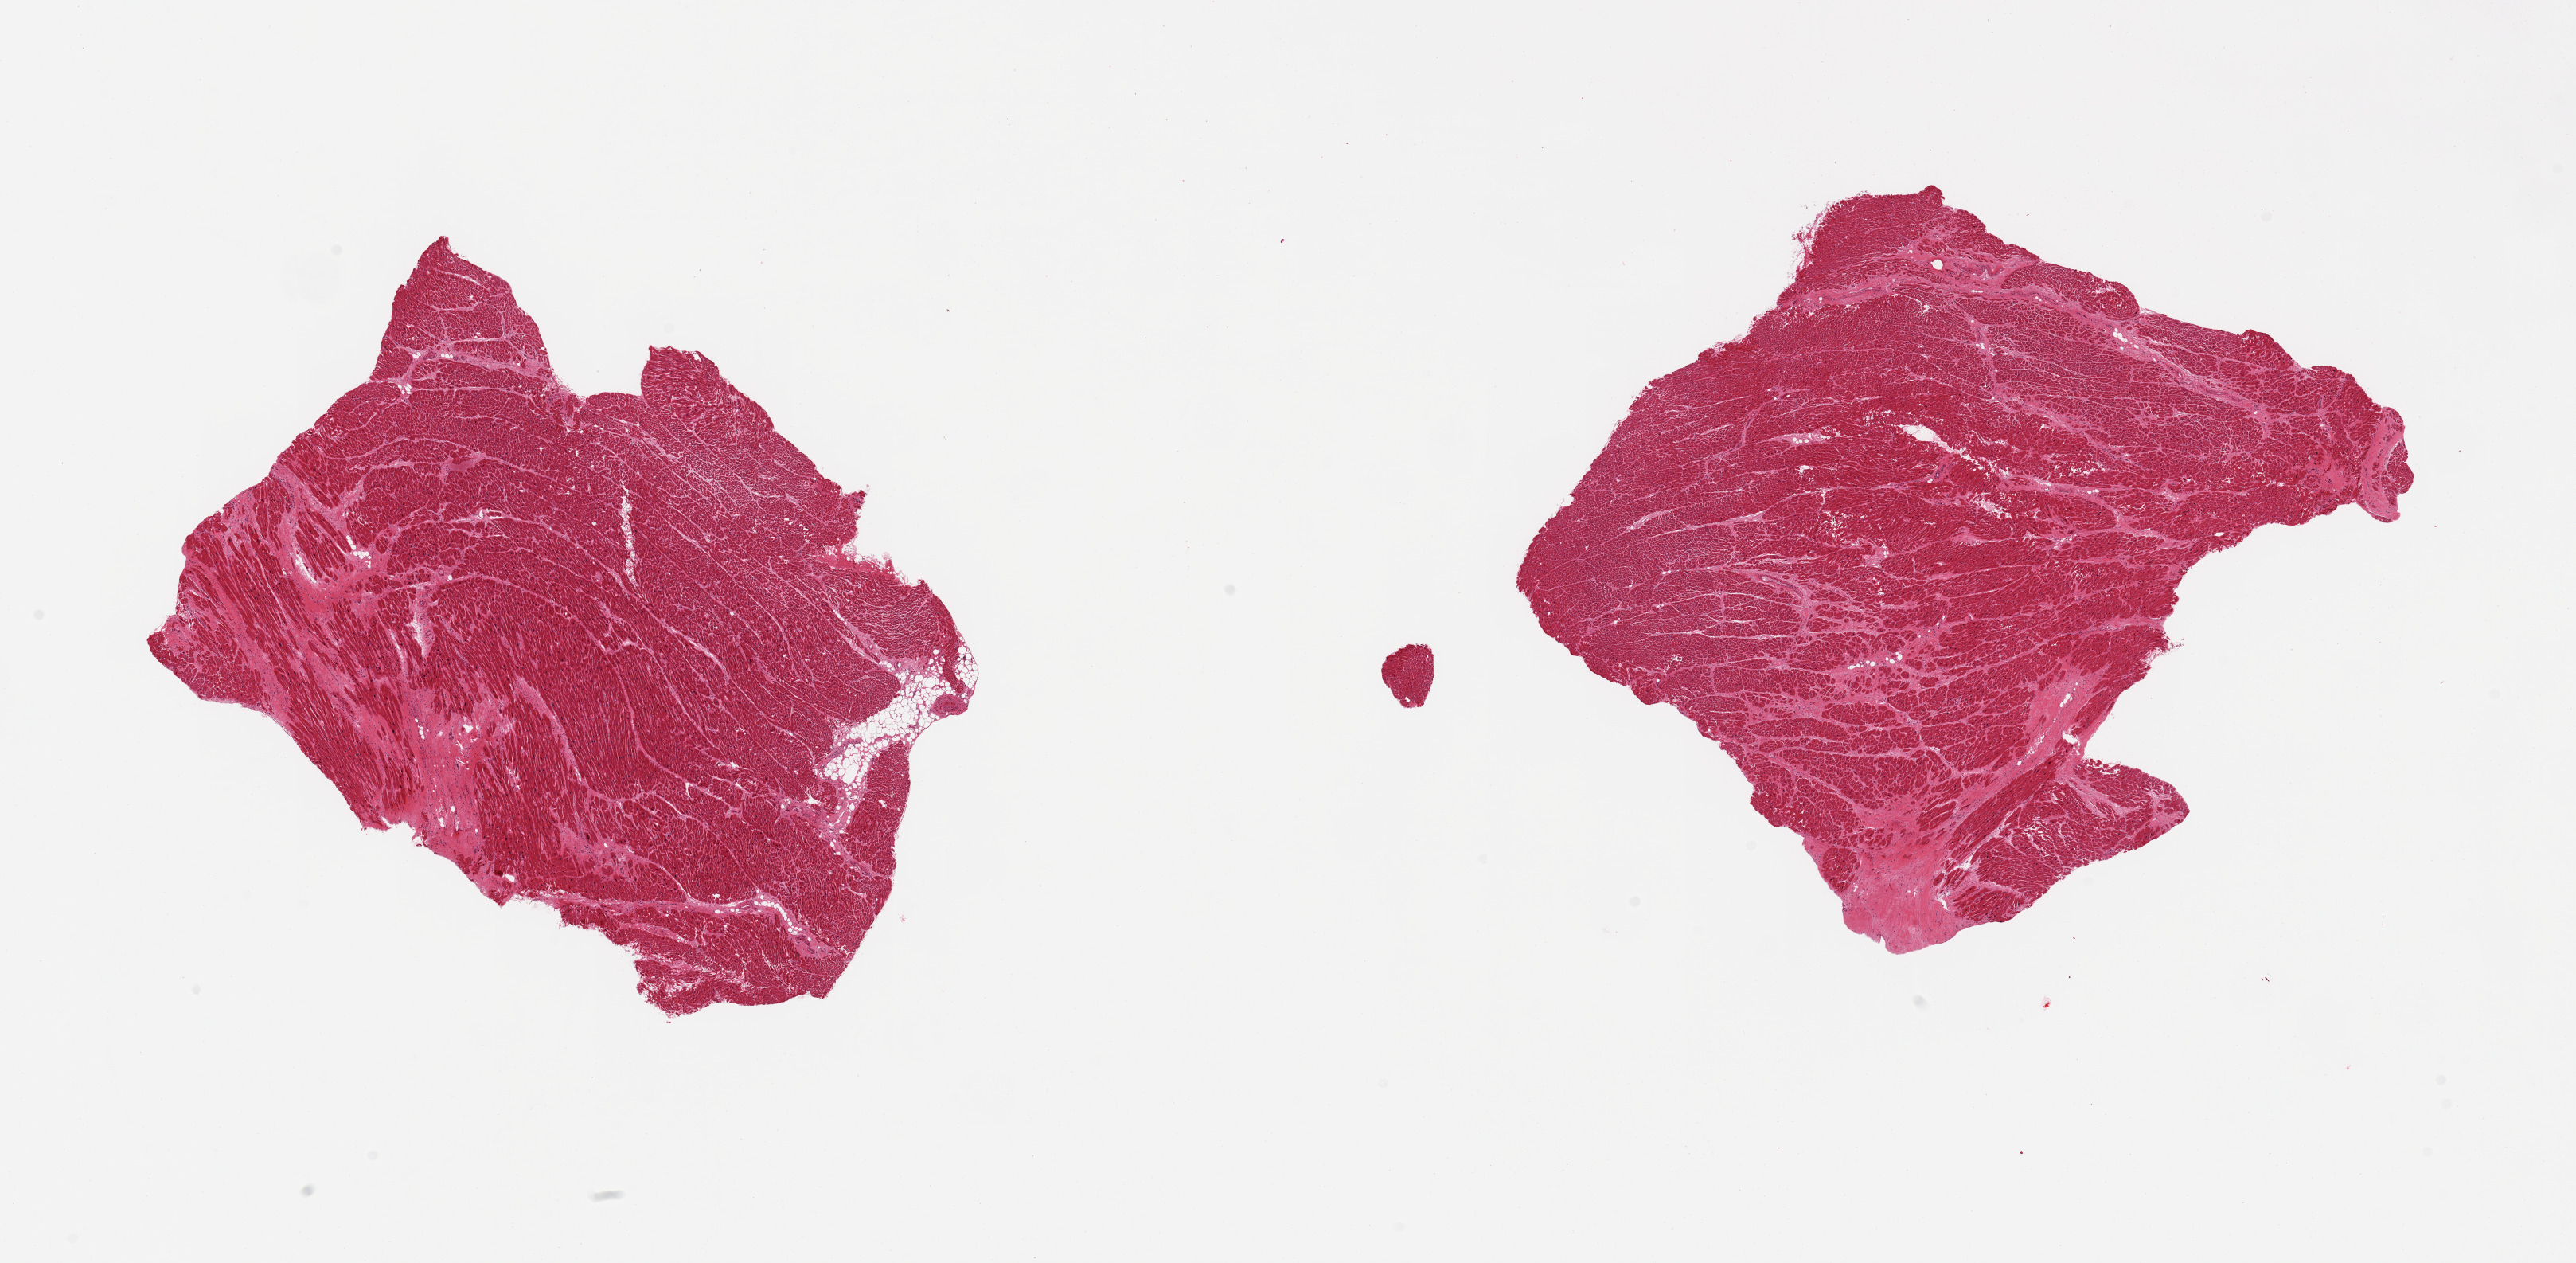
Whole-slide image, H&E stain, brightfield — shown as a low-resolution overview of the whole scanned area (about 25.6 x 12.5 mm), PAXgene-fixed, paraffin-embedded tissue, sampled site (target tissue): heart, donor tissue sample.
* reviewer comment on this tissue sample: 2 pieces, remote infarcts, moderate/marked chronic ischemic changes